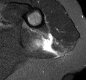
MRI of an extremity soft-tissue mass, one axial slice; slice 6 of 30 in the series (ordered by position); STIR; MR volume resampled by the dataset authors to the PET/CT grid (not the native acquisition matrix); 3.27 mm slice thickness; 86 × 80 image matrix. Female patient. Case-level facts recorded for this patient, not image findings: histological type: malignant fibrous histiocytoma; grade: low; site of the primary tumour: left arm.
Outlined on this slice (expert contour drawn on MRI and transferred to this co-registered scan by the dataset authors):
- gross tumour volume (mass): bounding box (x1, y1, x2, y2) in pixels: (33, 33, 52, 52)